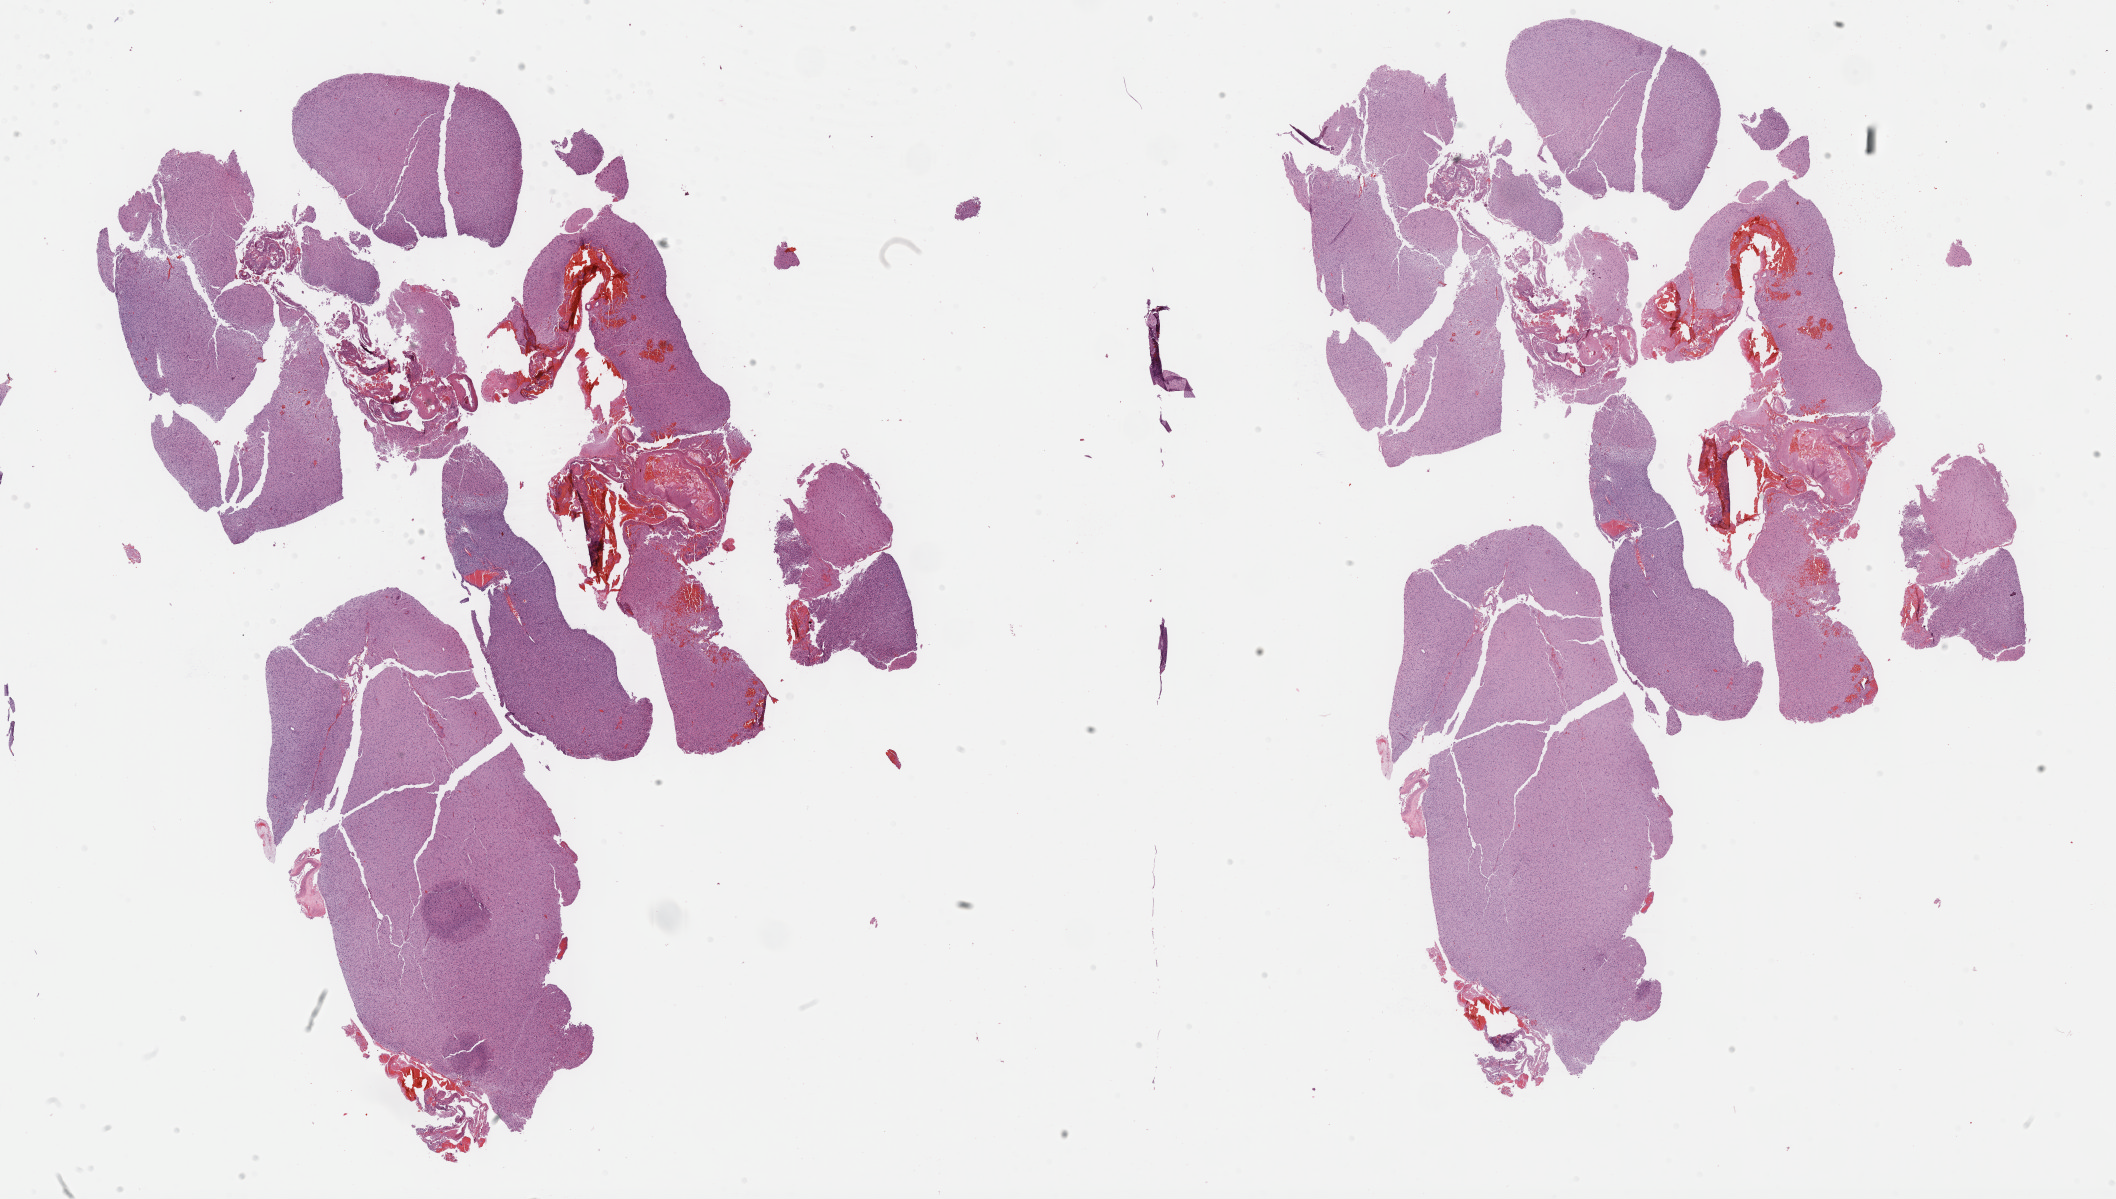
H&E whole-slide image, low-resolution overview of the scanned area, about 34.2 x 19.4 mm. Formalin-fixed paraffin-embedded (FFPE) diagnostic section. Primary tumour sample from the brain. Female patient; age at initial diagnosis 61 years. Histologic grade: G3 (poorly differentiated).
Pathologic diagnosis: Astrocytoma, anaplastic (cerebrum). Laterality: right.